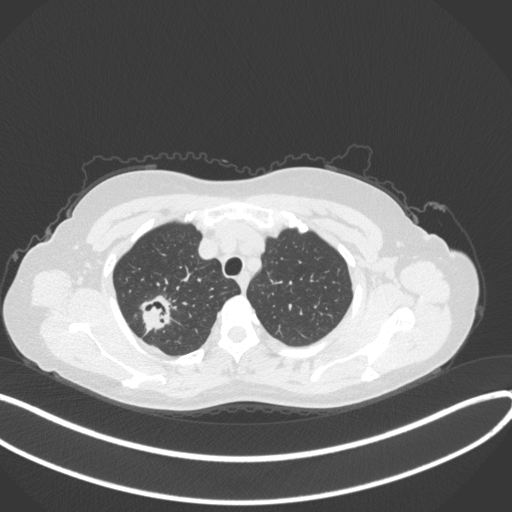
Chest CT, one axial slice; position 300 of 342 along the scan axis; reconstruction kernel B31f; 120 kVp; lung window (W 1500 / L -600 HU); 512 × 512 image matrix. Female patient, age 50 years. From the clinical record (not read from this slice): clinical TNM (as recorded): T1c N0 M0; histopathological grade: G2-3.
Structures marked on this image (rectangle marked by the reading radiologist):
- lung tumour (recorded histology: adenocarcinoma): bounding box <137,289,174,332> (left, top, right, bottom; pixels)